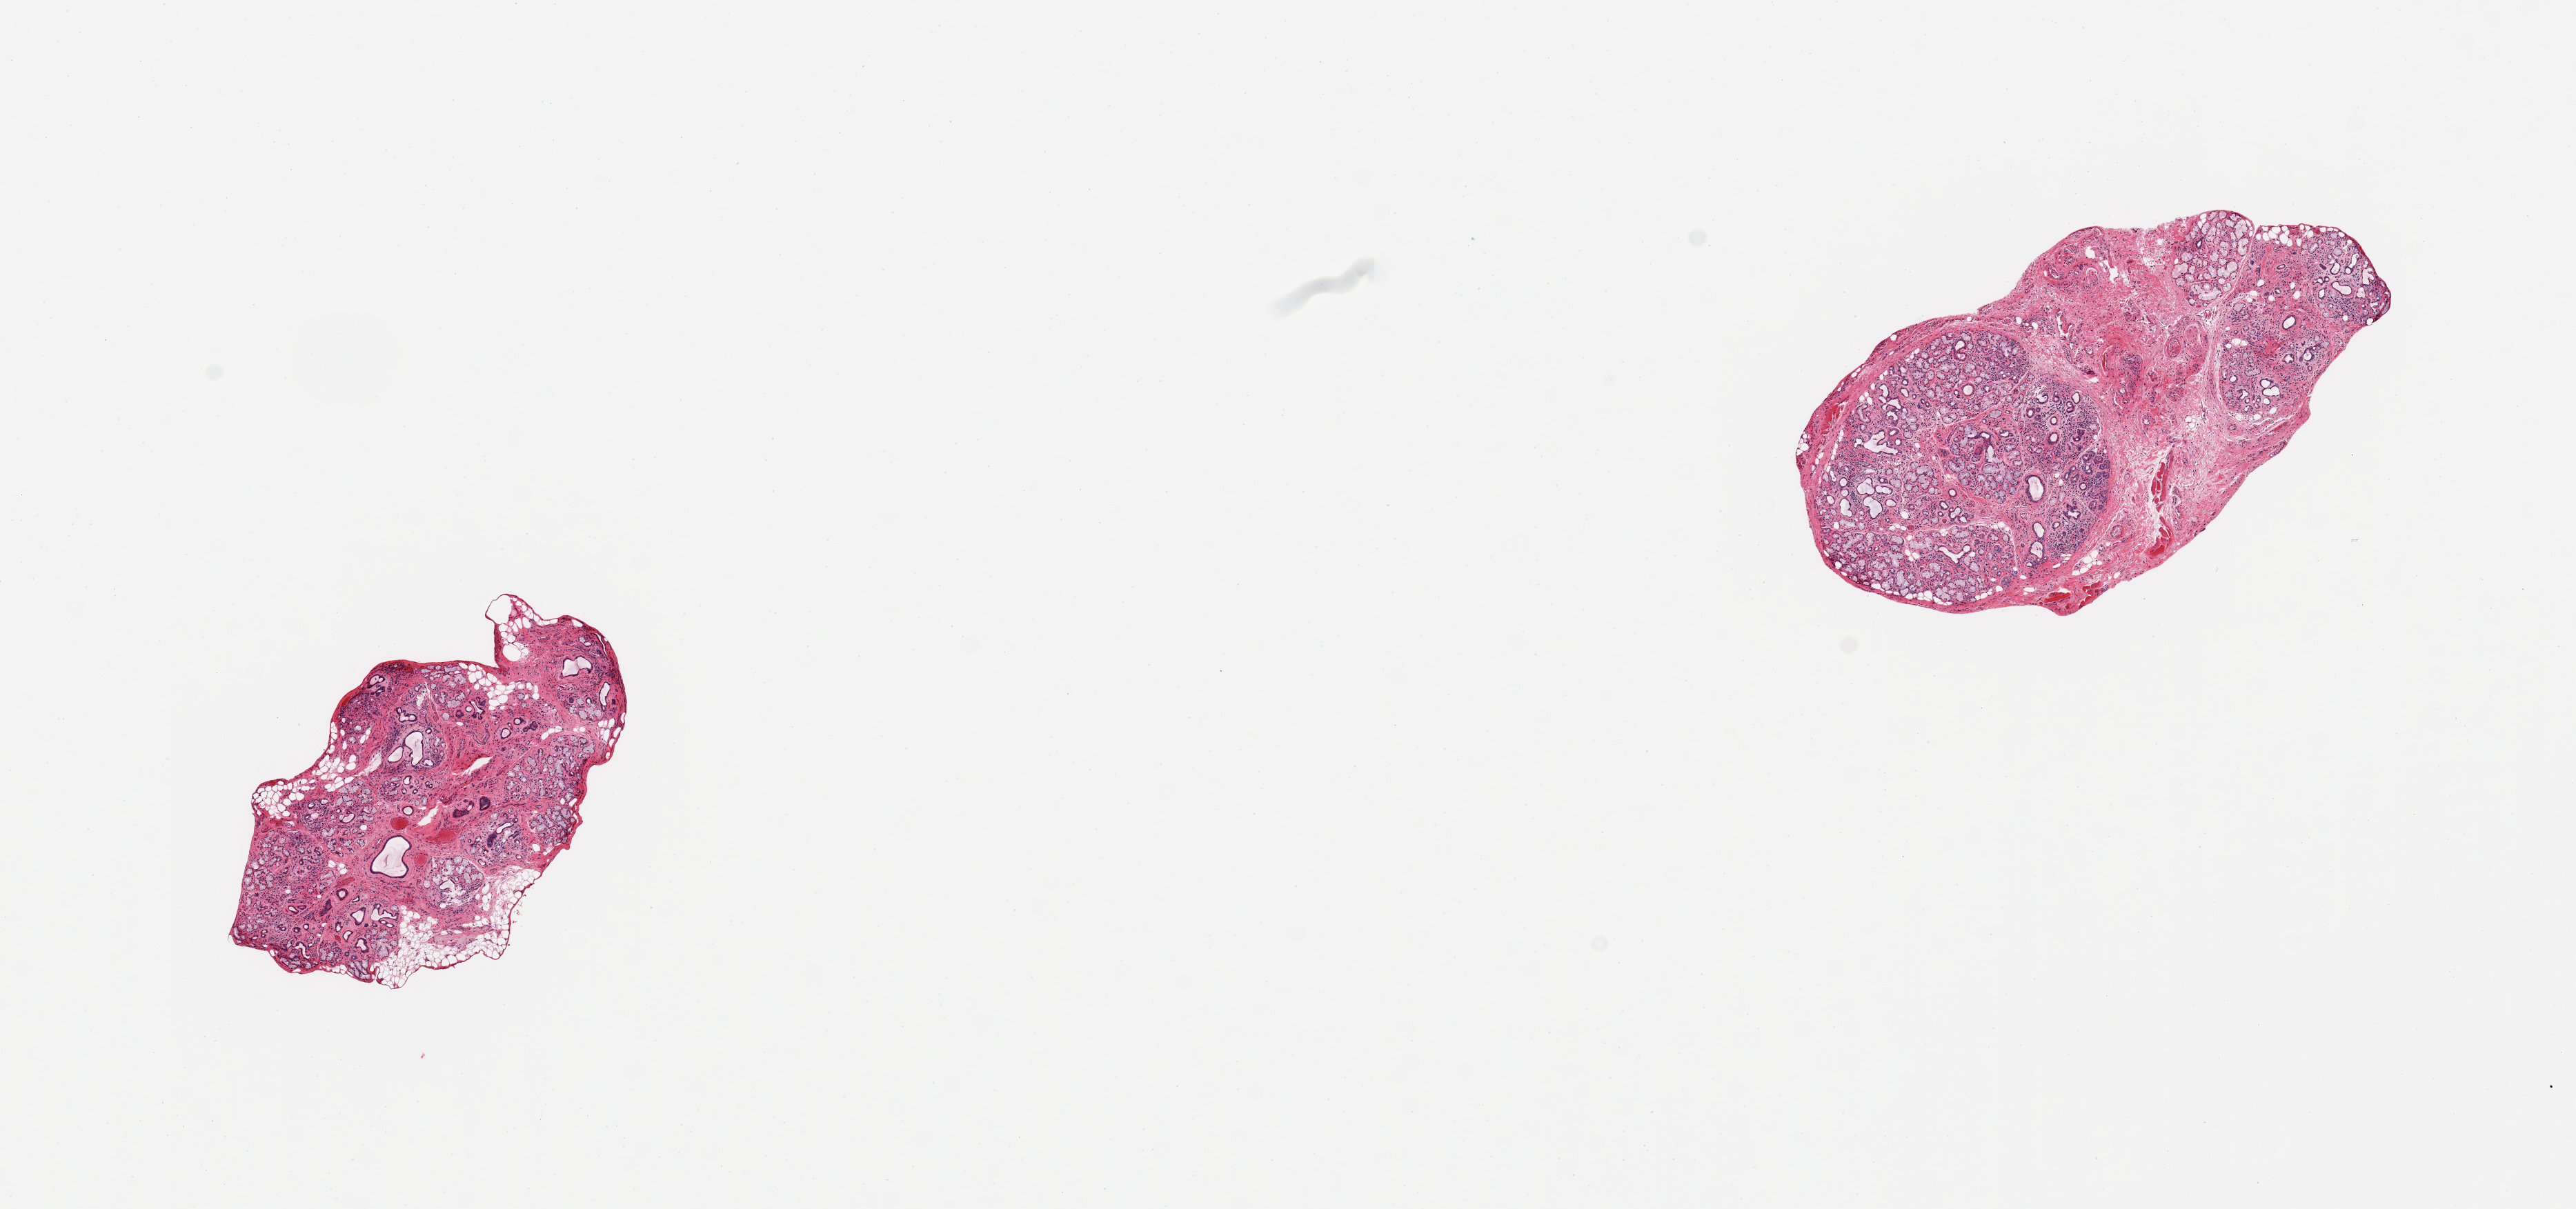
Whole-slide image, haematoxylin and eosin stain, brightfield, whole scanned area (about 14.8 x 6.9 mm, from a 20x scan) shown as a low-resolution overview; PAXgene-fixed, paraffin-embedded tissue; target tissue: minor salivary gland; tissue donor sample.
Review note (as recorded): 2 pieces; mild to moderate atrophy with fibrosis and ductal dilatation; 30% external fibrous and fatty content.